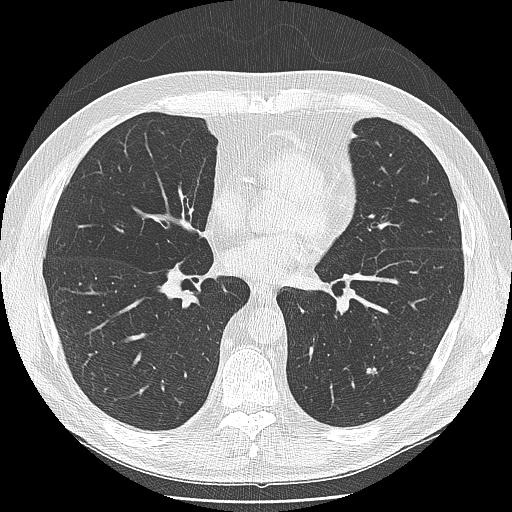
Low-dose screening chest CT, one axial slice. Position 79 of 166 along the scan axis. 120 kVp. Lung window (W 1500 / L -600 HU). 2.5 mm slice thickness. 512 × 512 image matrix.
Outlined on this slice (outlined manually by an expert reader):
- lesion 1 (tumor, lower lobe of left lung): bounding box <366,367,378,375> (left, top, right, bottom; pixels)